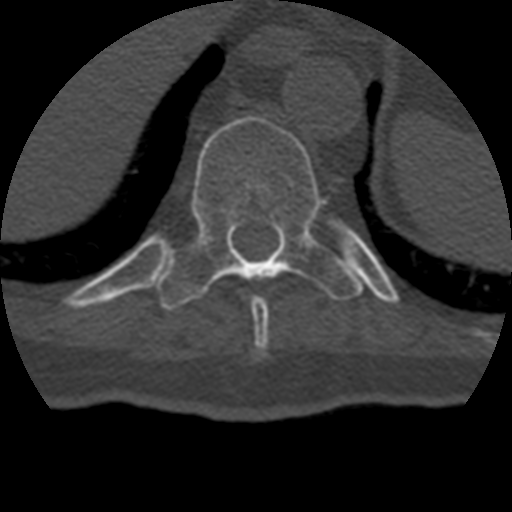
CT including the spine, one axial slice. Position 223 of 399 along the scan axis. 120 kVp. Bone window (W 1800 / L 400 HU). 1.25 mm slice thickness. 512 × 512 image matrix, field of view 160 × 160 mm. Patient age 69 years. Case-level facts recorded for this patient, not image findings: primary cancer: prostate.
Outlined on this slice (semi-automatically segmented with operator editing):
- T10 vertebra: bounding box (x1, y1, x2, y2) in pixels: (157, 116, 363, 310)
- T9 vertebra: (251, 295, 270, 353)